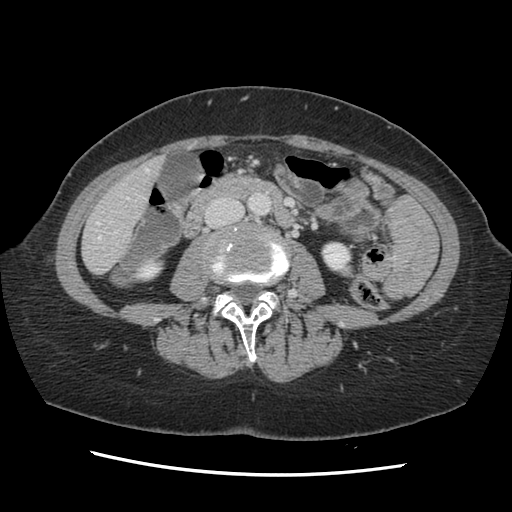
Contrast-enhanced abdominal CT, one axial slice. Soft-tissue window (W 400 / L 40 HU). 2.5 mm slice thickness. 512 × 512 image matrix, field of view 330 × 330 mm. Female patient, age 61 years. From the clinical record (not read from this slice): diagnosis: colorectal cancer liver metastases, imaged before liver resection; multiple liver metastases: no; largest metastasis: 2.4 cm; chemotherapy before resection: no.
Outlined on this slice (outlined manually by an expert reader):
- hepatic veins: bounding box [x1, y1, x2, y2] px = [97, 169, 149, 239]
- liver: [84, 160, 161, 274]
- planned liver remnant (the part of the liver to remain after resection): [84, 162, 161, 274]